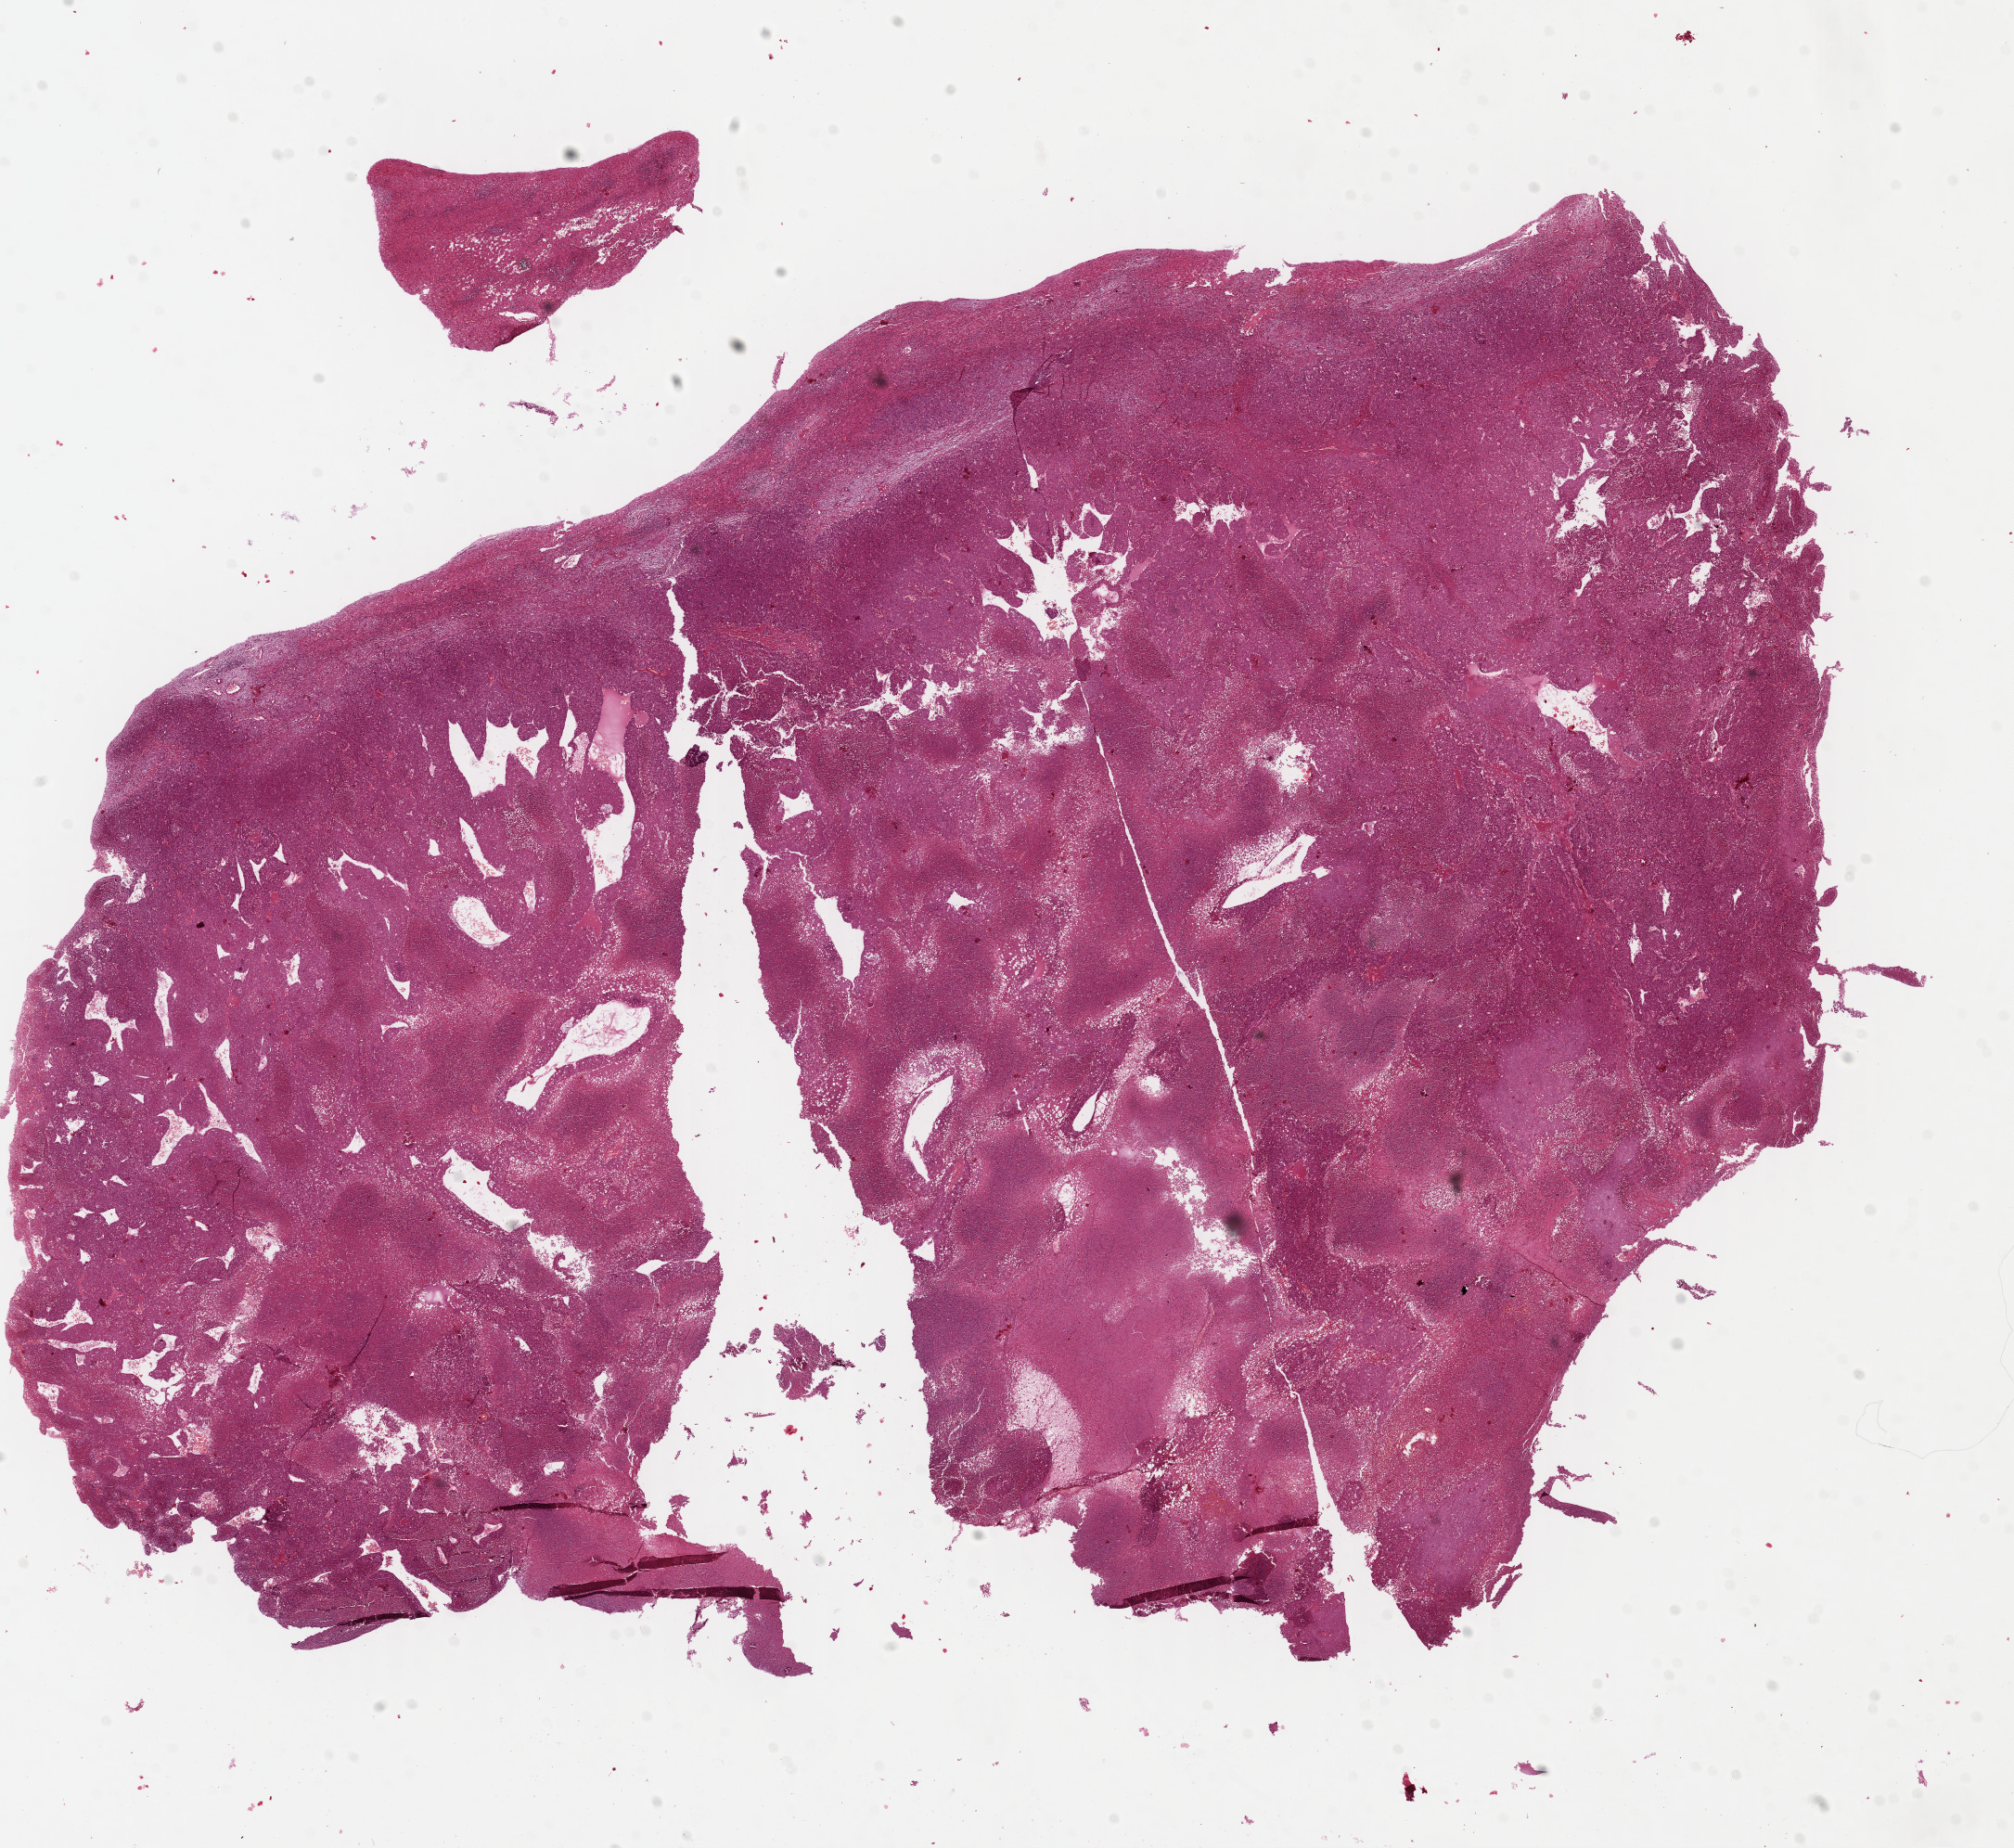
Digitized H&E-stained tissue section (whole slide), low-resolution overview of the scanned area, about 17.1 x 15.7 mm (from a 40x scan), formalin-fixed paraffin-embedded (FFPE) diagnostic section, sample: primary tumour, liver. Male patient; age at initial diagnosis 35 years. Histologic grade: G1 (well differentiated).
Diagnosis: Hepatocellular carcinoma, NOS. AJCC pathologic stage: IIIA.